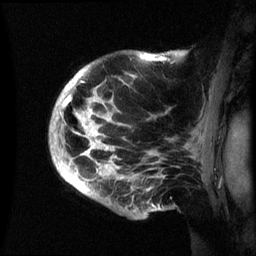
Breast MRI (dynamic contrast-enhanced), one sagittal slice. Position 47 of 60 along the scan axis. Dynamic contrast-enhanced series, image 2 of 3 at this slice position (ordered by acquisition). 1.5 T. TE 4.2 ms, TR 8.4 ms. 2.4 mm slice thickness. 256 × 256 image matrix. Female patient, age 48 years.
Annotated regions visible in this slice (semi-automatic segmentation, software-assisted and operator-edited):
- analysis volume of interest (the breast-tissue region the enhancement analysis was run in; not a lesion): bounding box <50,51,195,219> (left, top, right, bottom; pixels)
- tumour enhancement mask (voxels above the 70 % enhancement threshold inside the analysis volume of interest): <60,55,155,181>